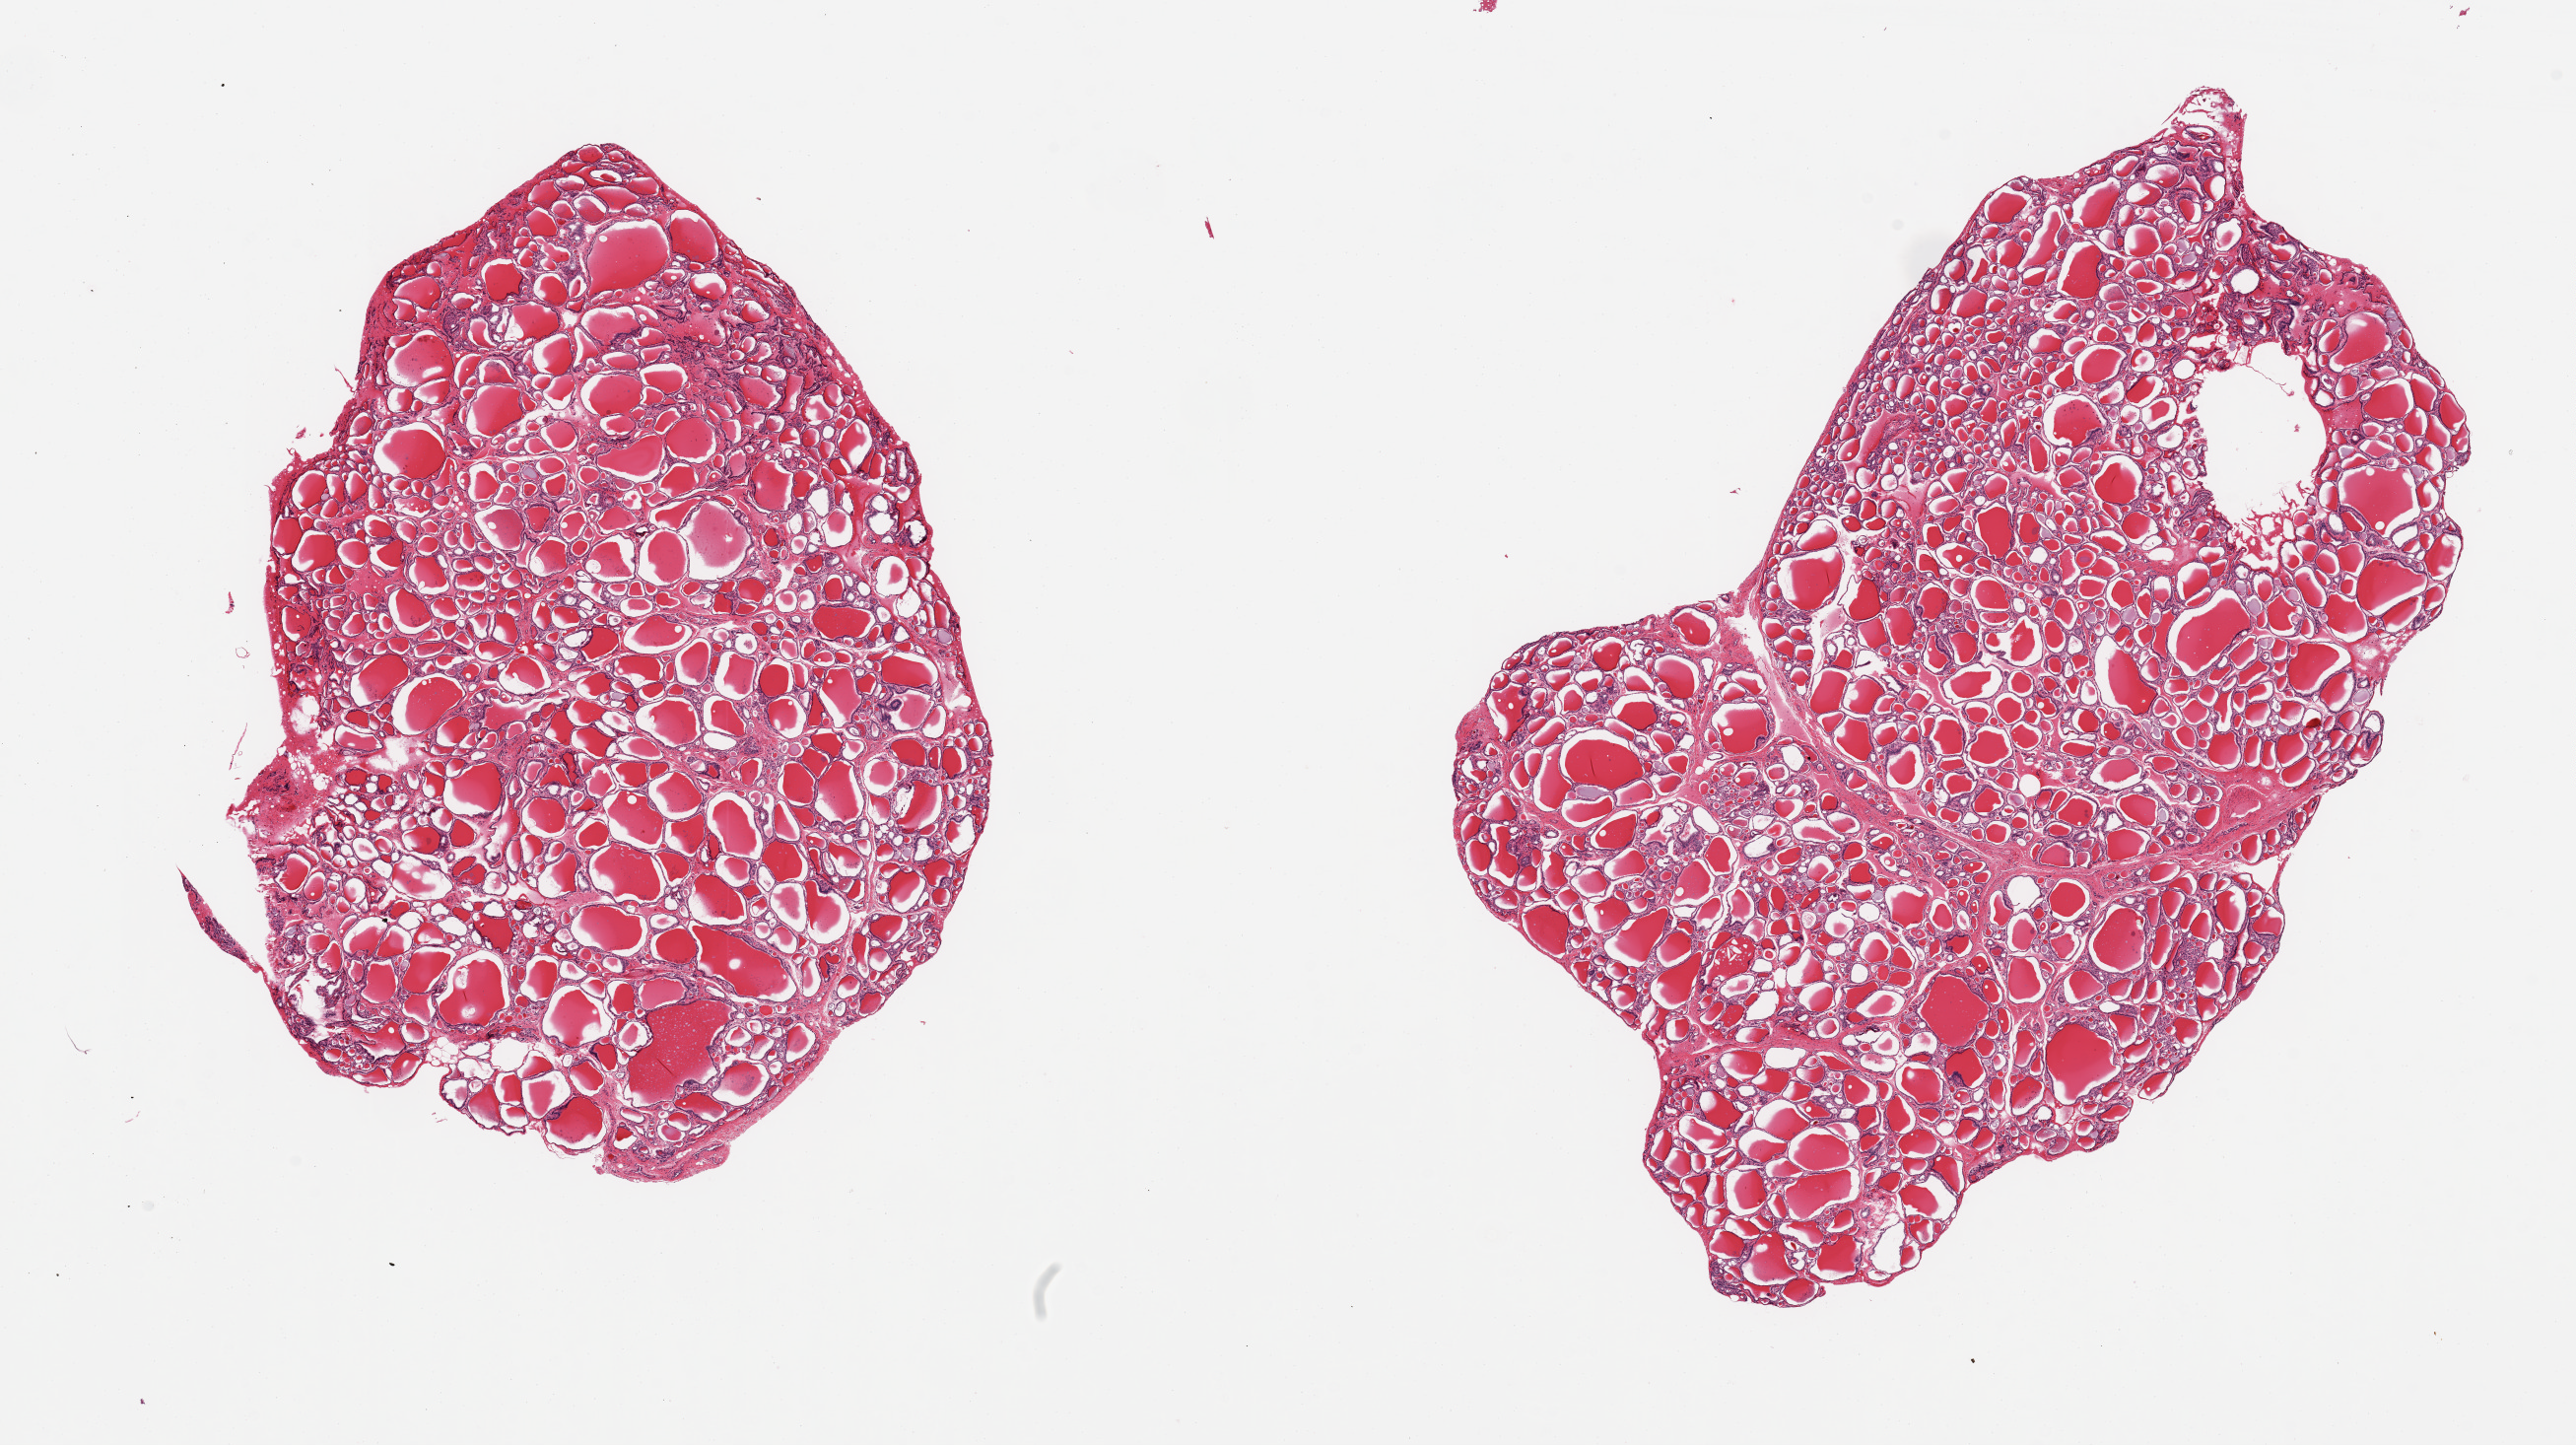
Haematoxylin and eosin whole-slide image — shown as a low-resolution overview of the whole scanned area (about 20.7 x 11.6 mm), PAXgene-fixed, paraffin-embedded tissue, section of thyroid (target tissue), tissue donor sample. Donor: male.
• reviewer comment on this tissue sample: 2 pieces; well dissected; no extraneous tissue